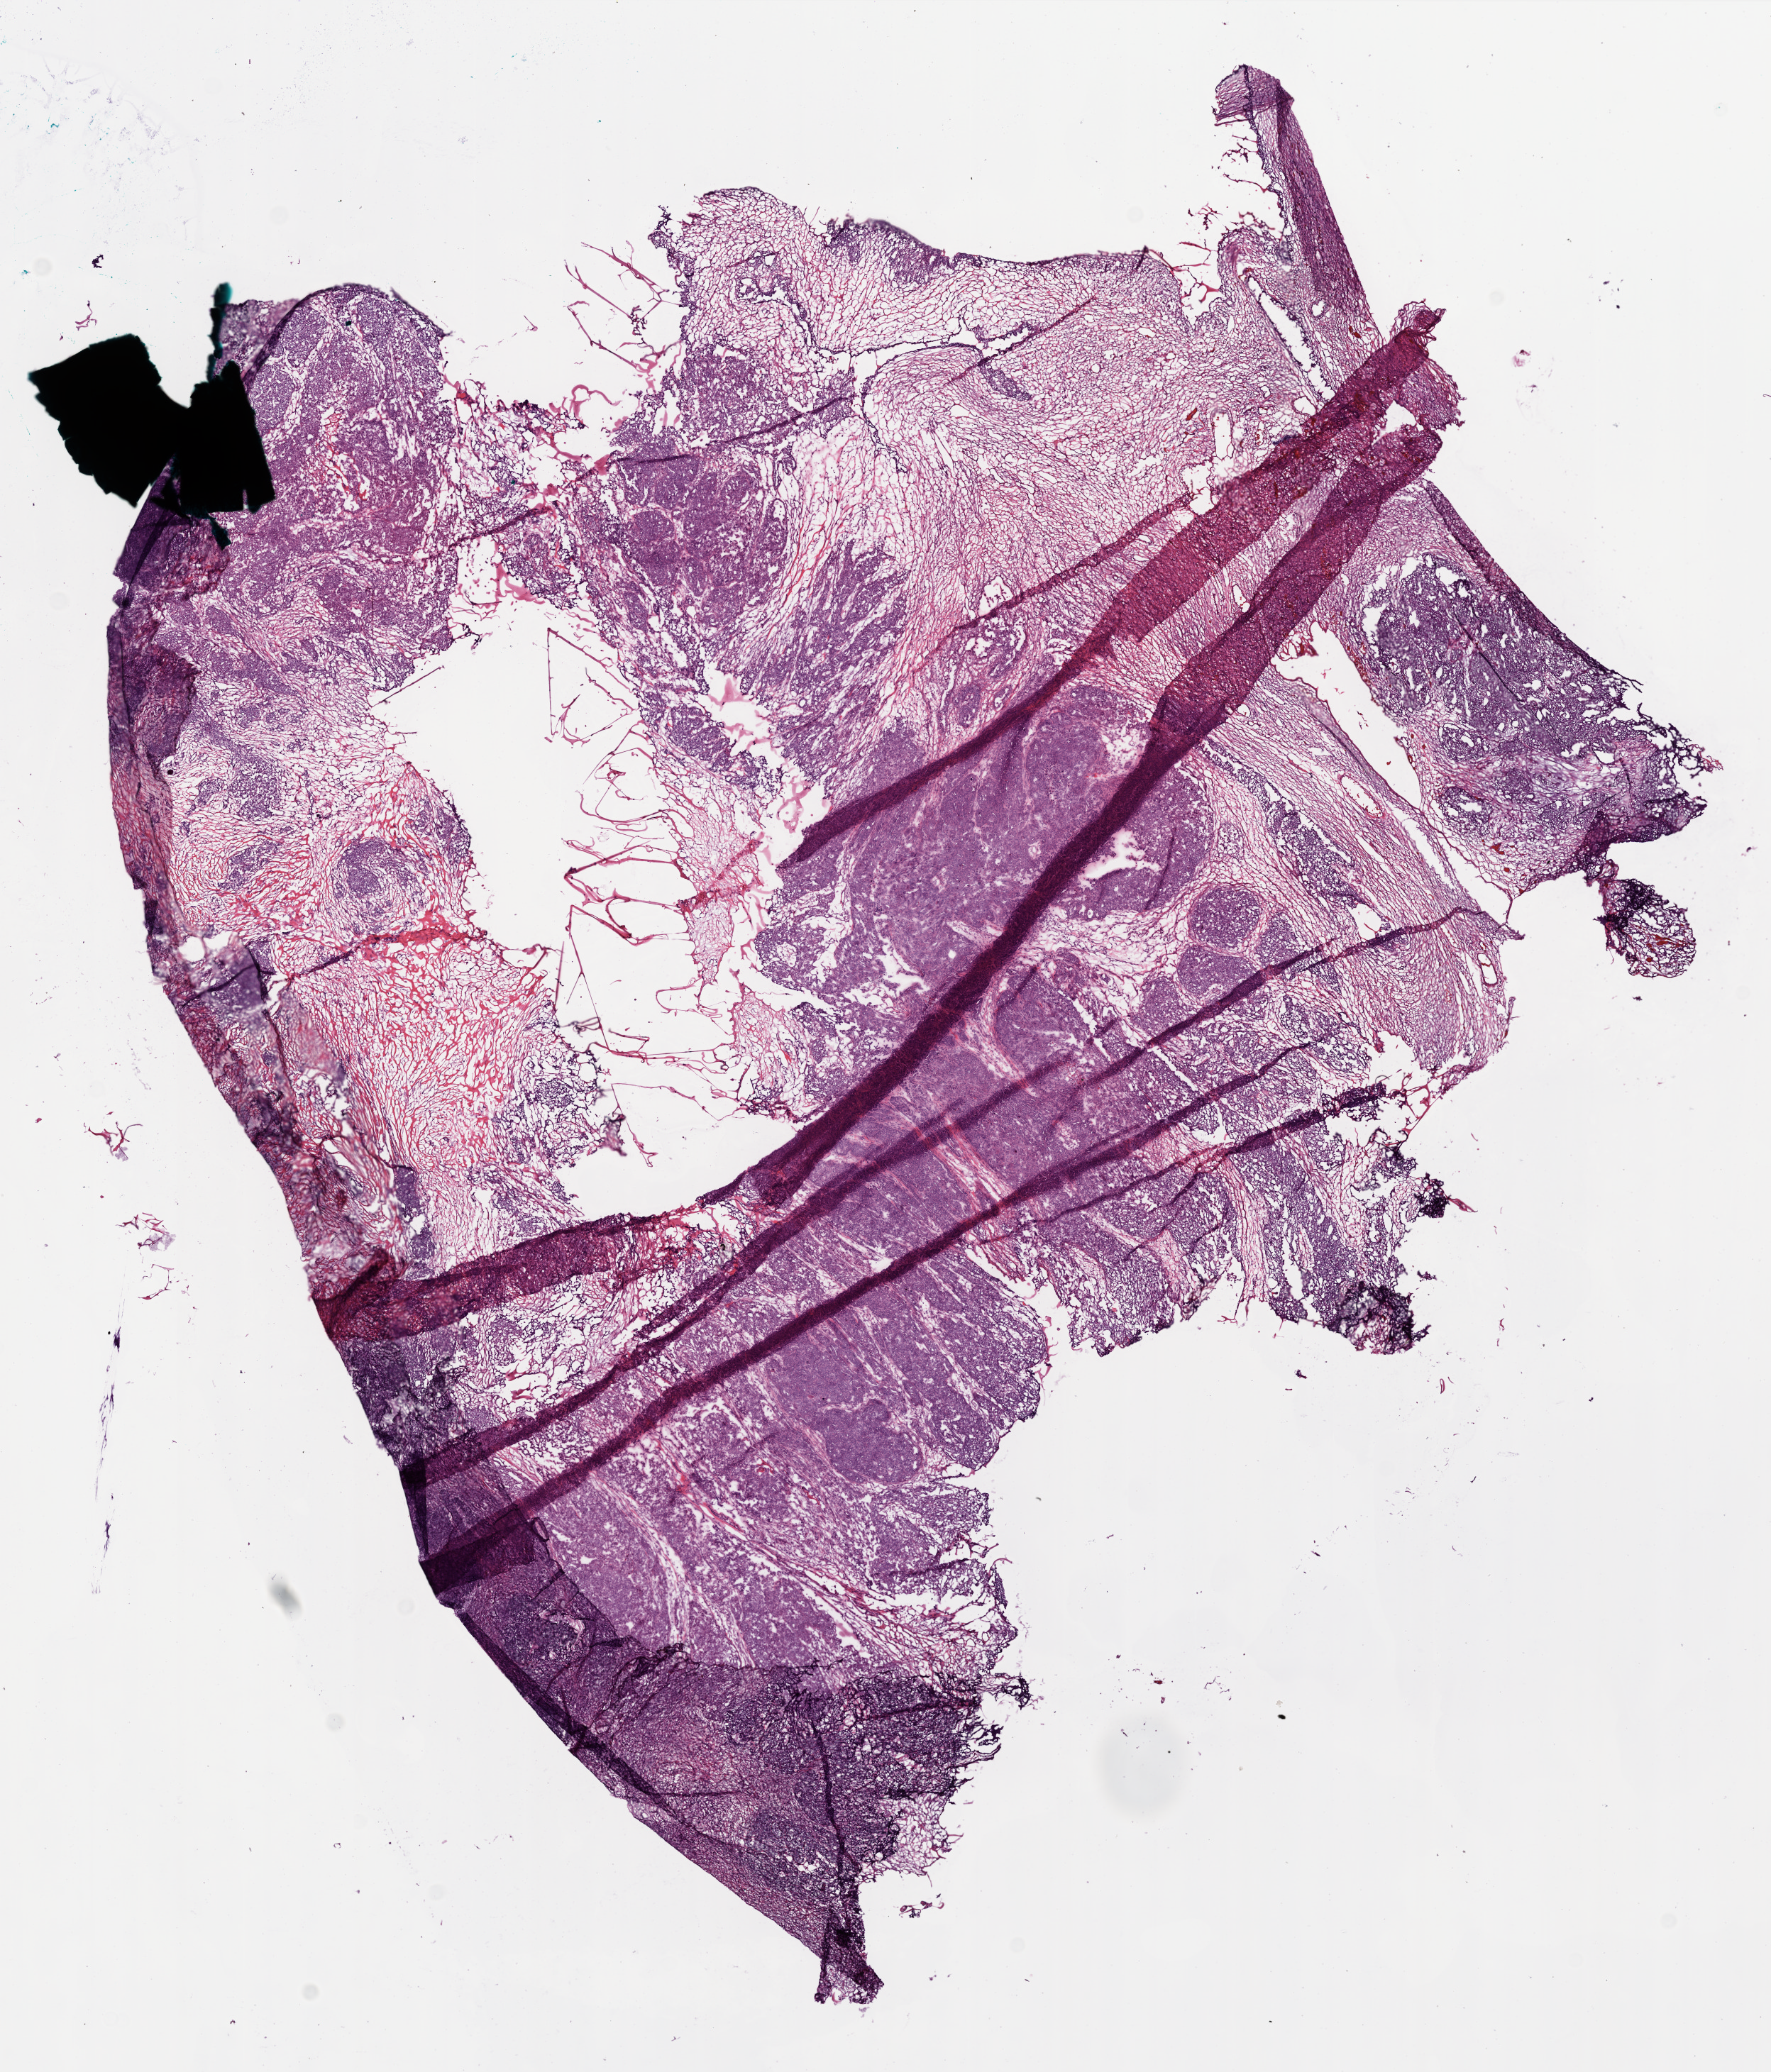
Digitized Hematoxylin and eosin (H&E) stained tissue section (whole slide) — a low-resolution overview of the entire scanned area, about 10.0 x 11.7 mm (slide scanned at 20x), frozen section, ovary, primary tumour sample. Female, age 60 years at initial diagnosis. Histologic grade: G3 (poorly differentiated). Pathologist review of this section (percent, as recorded): tumour cells 0%, tumour nuclei 95%, normal cells 0%, stromal cells 0%, necrosis 10%.
FIGO stage: IIIC. Laterality: right. Diagnosis: Serous cystadenocarcinoma, NOS.